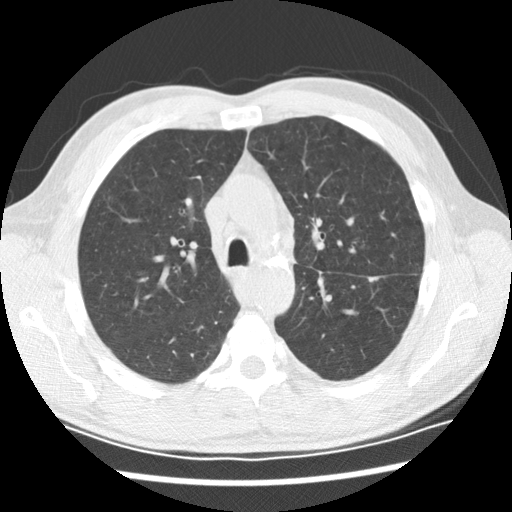
Low-dose screening chest CT, one axial slice. Position 140 of 208 along the scan axis. Reconstruction kernel STANDARD. 120 kVp. Lung window (W 1500 / L -600 HU). 2.5 mm slice thickness. 512 × 512 image matrix, field of view 340 × 340 mm.
Outlined on this slice (outlined manually by an expert reader):
- lesion 2 (tumor, lower lobe of left lung): bounding box [x1, y1, x2, y2] px = [368, 277, 379, 282]